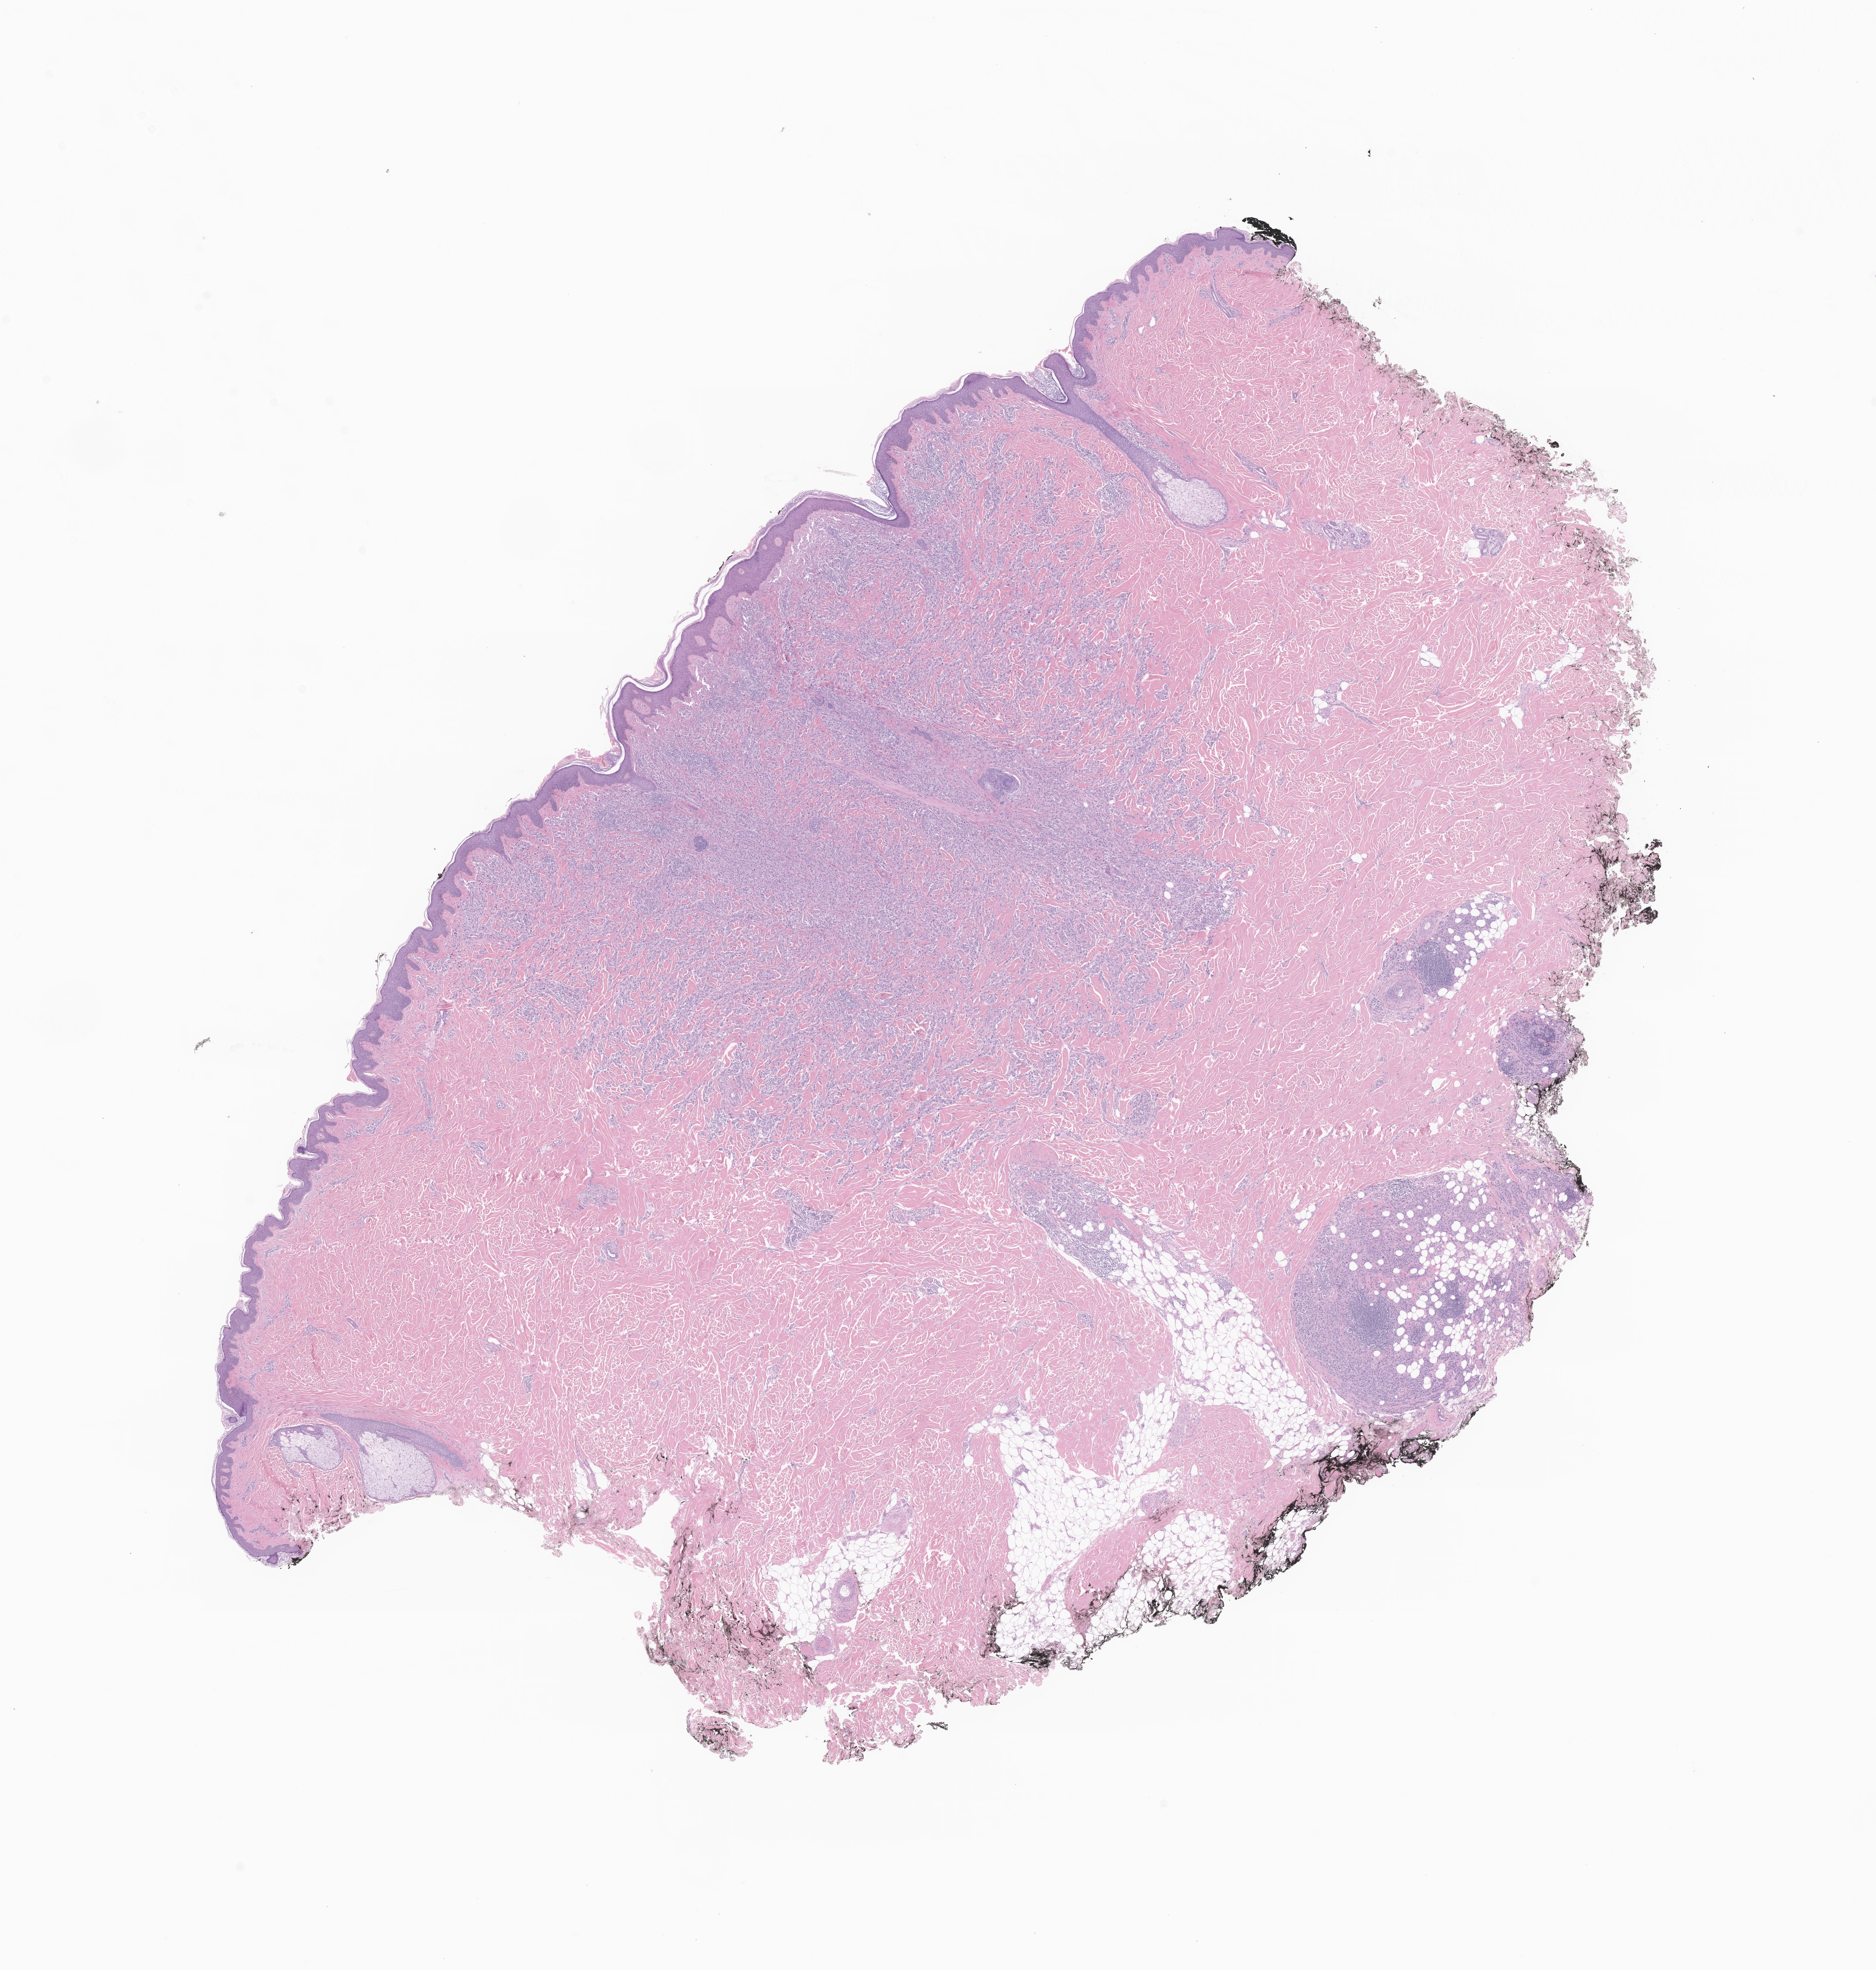
Digitized haematoxylin and eosin-stained section of tumor tissue from the skin of trunk — shown as a low-resolution overview of the whole scanned area (about 16.4 x 17.2 mm); formalin-fixed, paraffin-embedded (FFPE) tissue. Patient male; age 171 months (14 years 3 months).
- diagnosis: Nodular melanoma